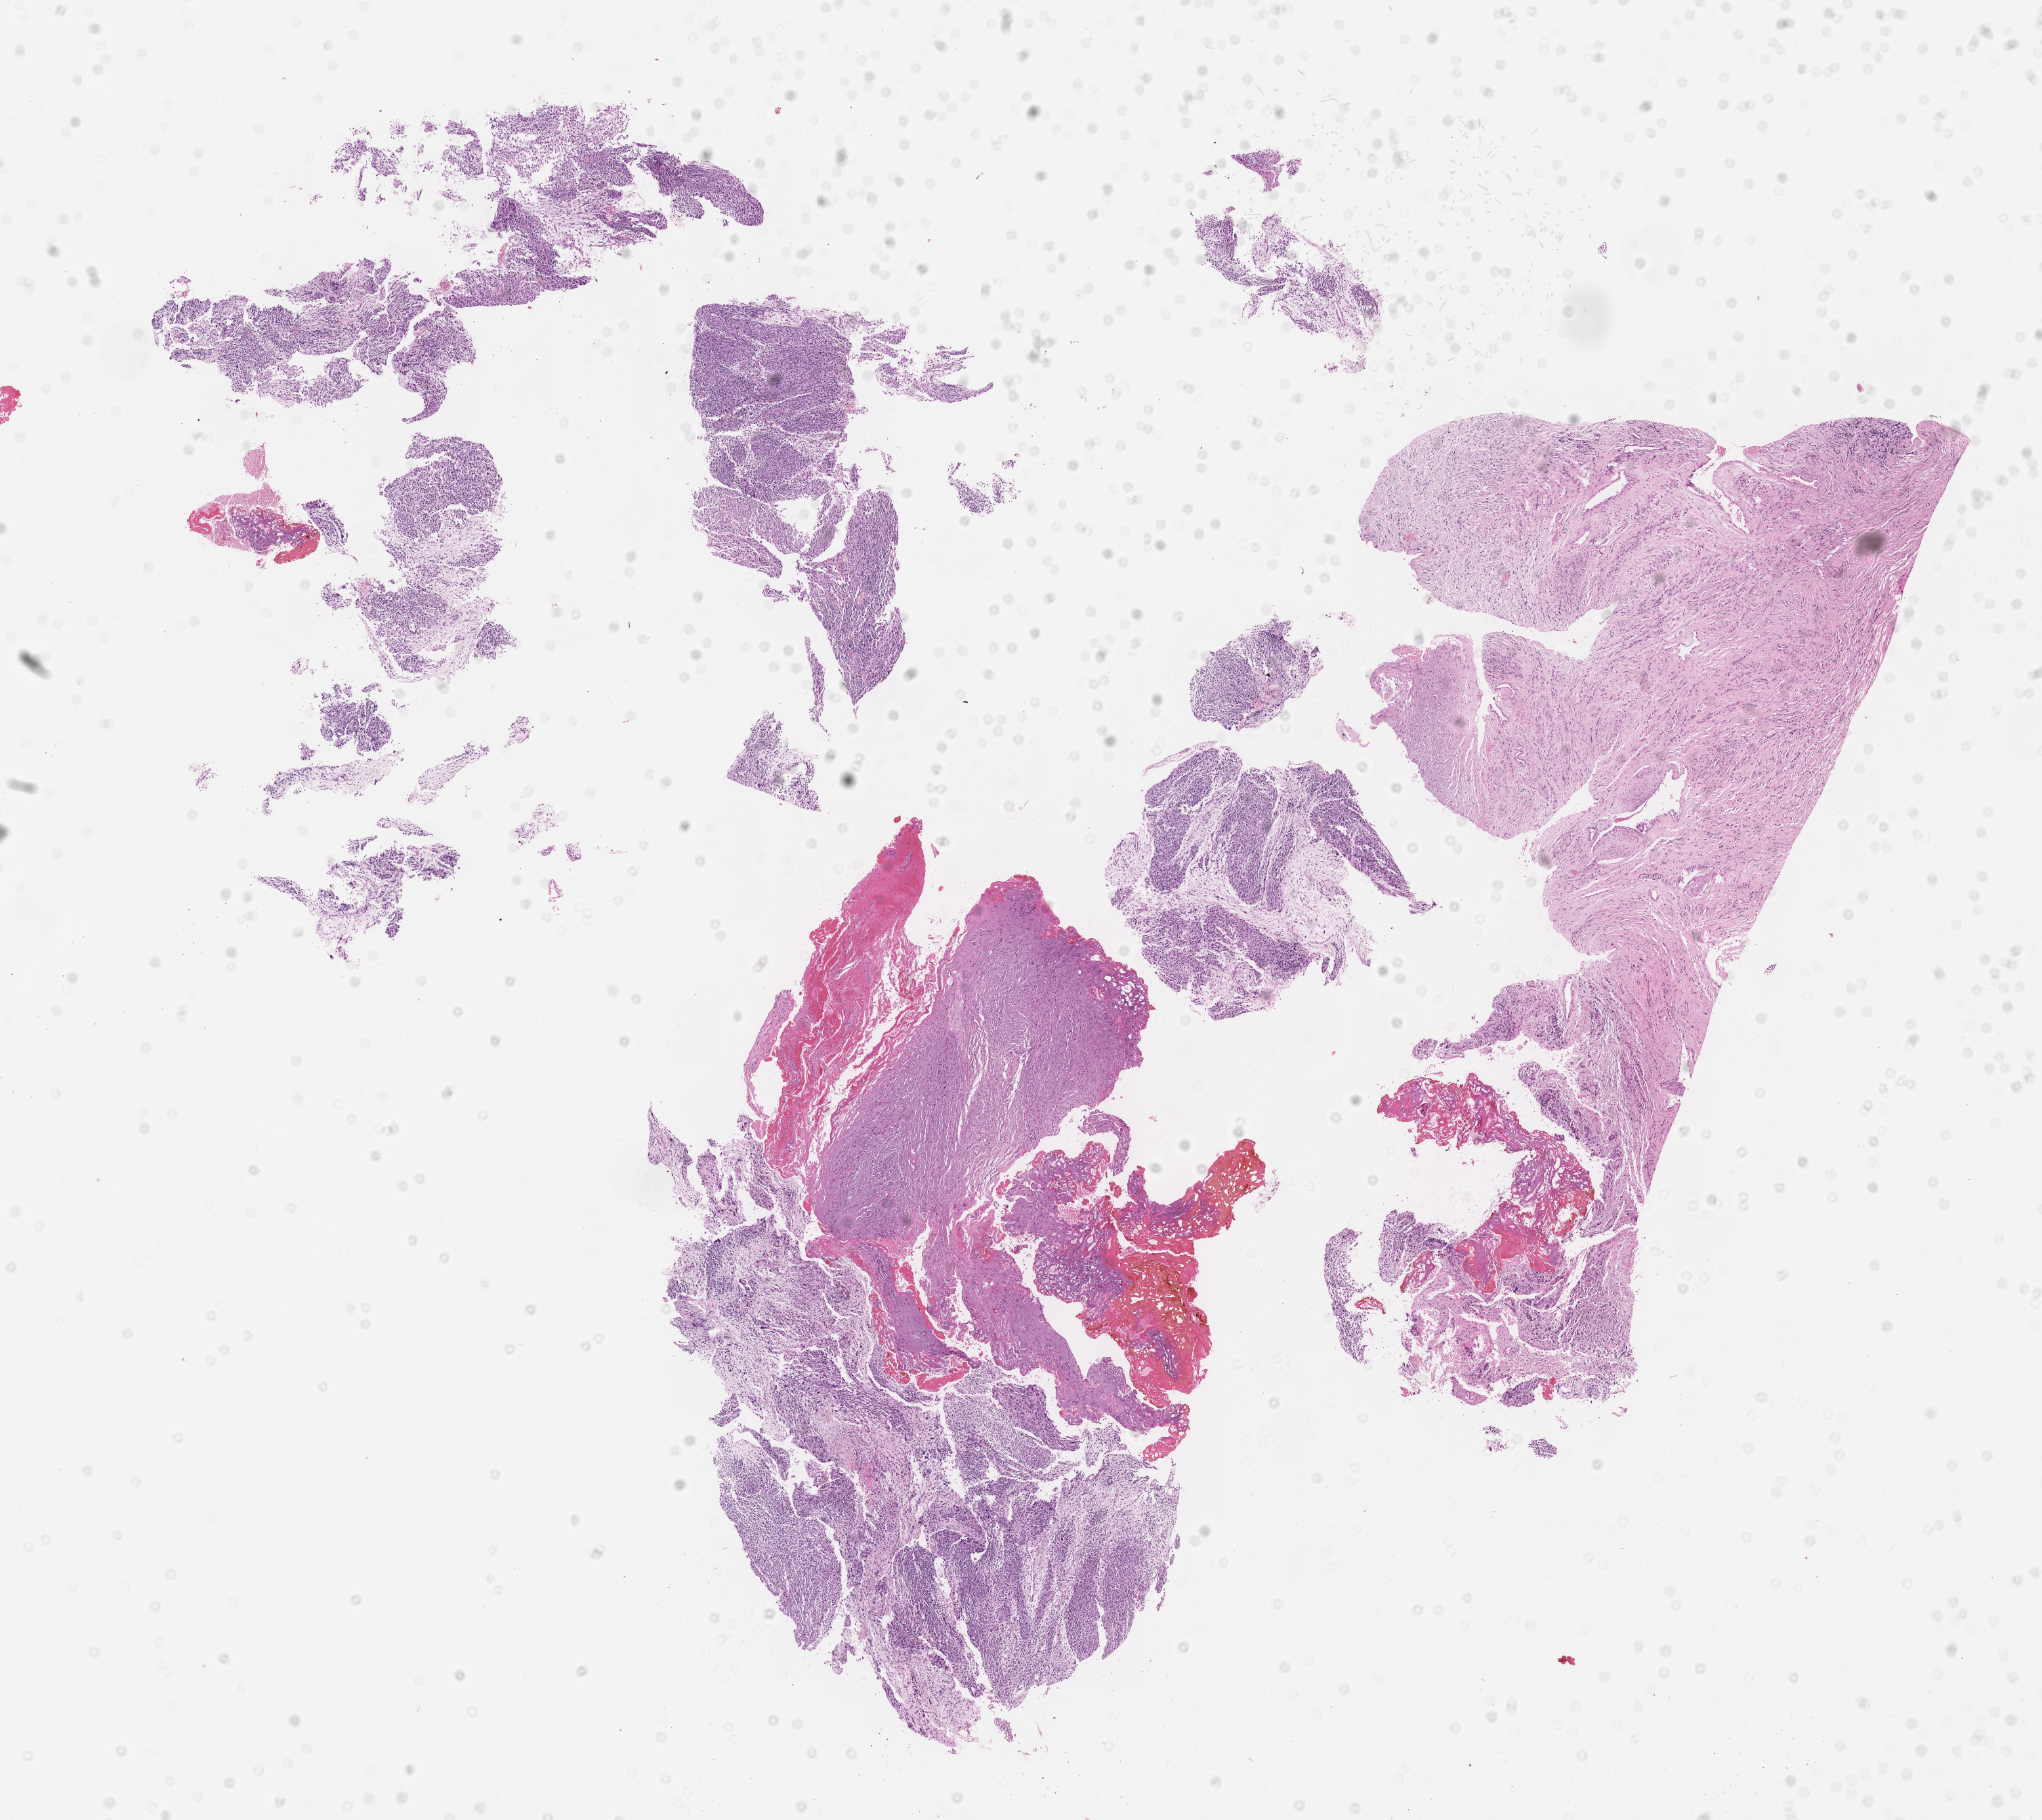
Whole-slide image, H&E stain of tumor tissue — whole scanned area (about 12.6 x 11.2 mm) shown as a low-resolution overview; formalin-fixed paraffin-embedded section; sample anatomic site: soft tissue, abdomen. Patient: male, age 0.0 years at diagnosis.
* stage (as recorded): 3
* diagnosis: rhabdomyosarcoma; histological classification: embryonal rhabdomyosarcoma
* metastatic status at presentation (as recorded): non-metastatic